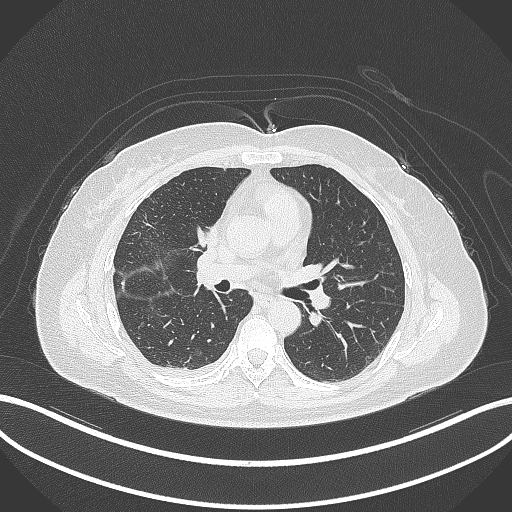
Chest CT, one axial slice; slice 150 of 305 in the series (ordered by position); 120 kVp; lung window (W 1500 / L -600 HU); 1 mm slice thickness; 512 × 512 image matrix. Female patient, age 52 years. Case-level facts recorded for this patient, not image findings: clinical TNM (as recorded): T3 N1 M1.
Annotated regions visible in this slice (rectangle marked by the reading radiologist):
- lung tumour (recorded histology: adenocarcinoma): bounding box <190,222,221,253> (left, top, right, bottom; pixels)